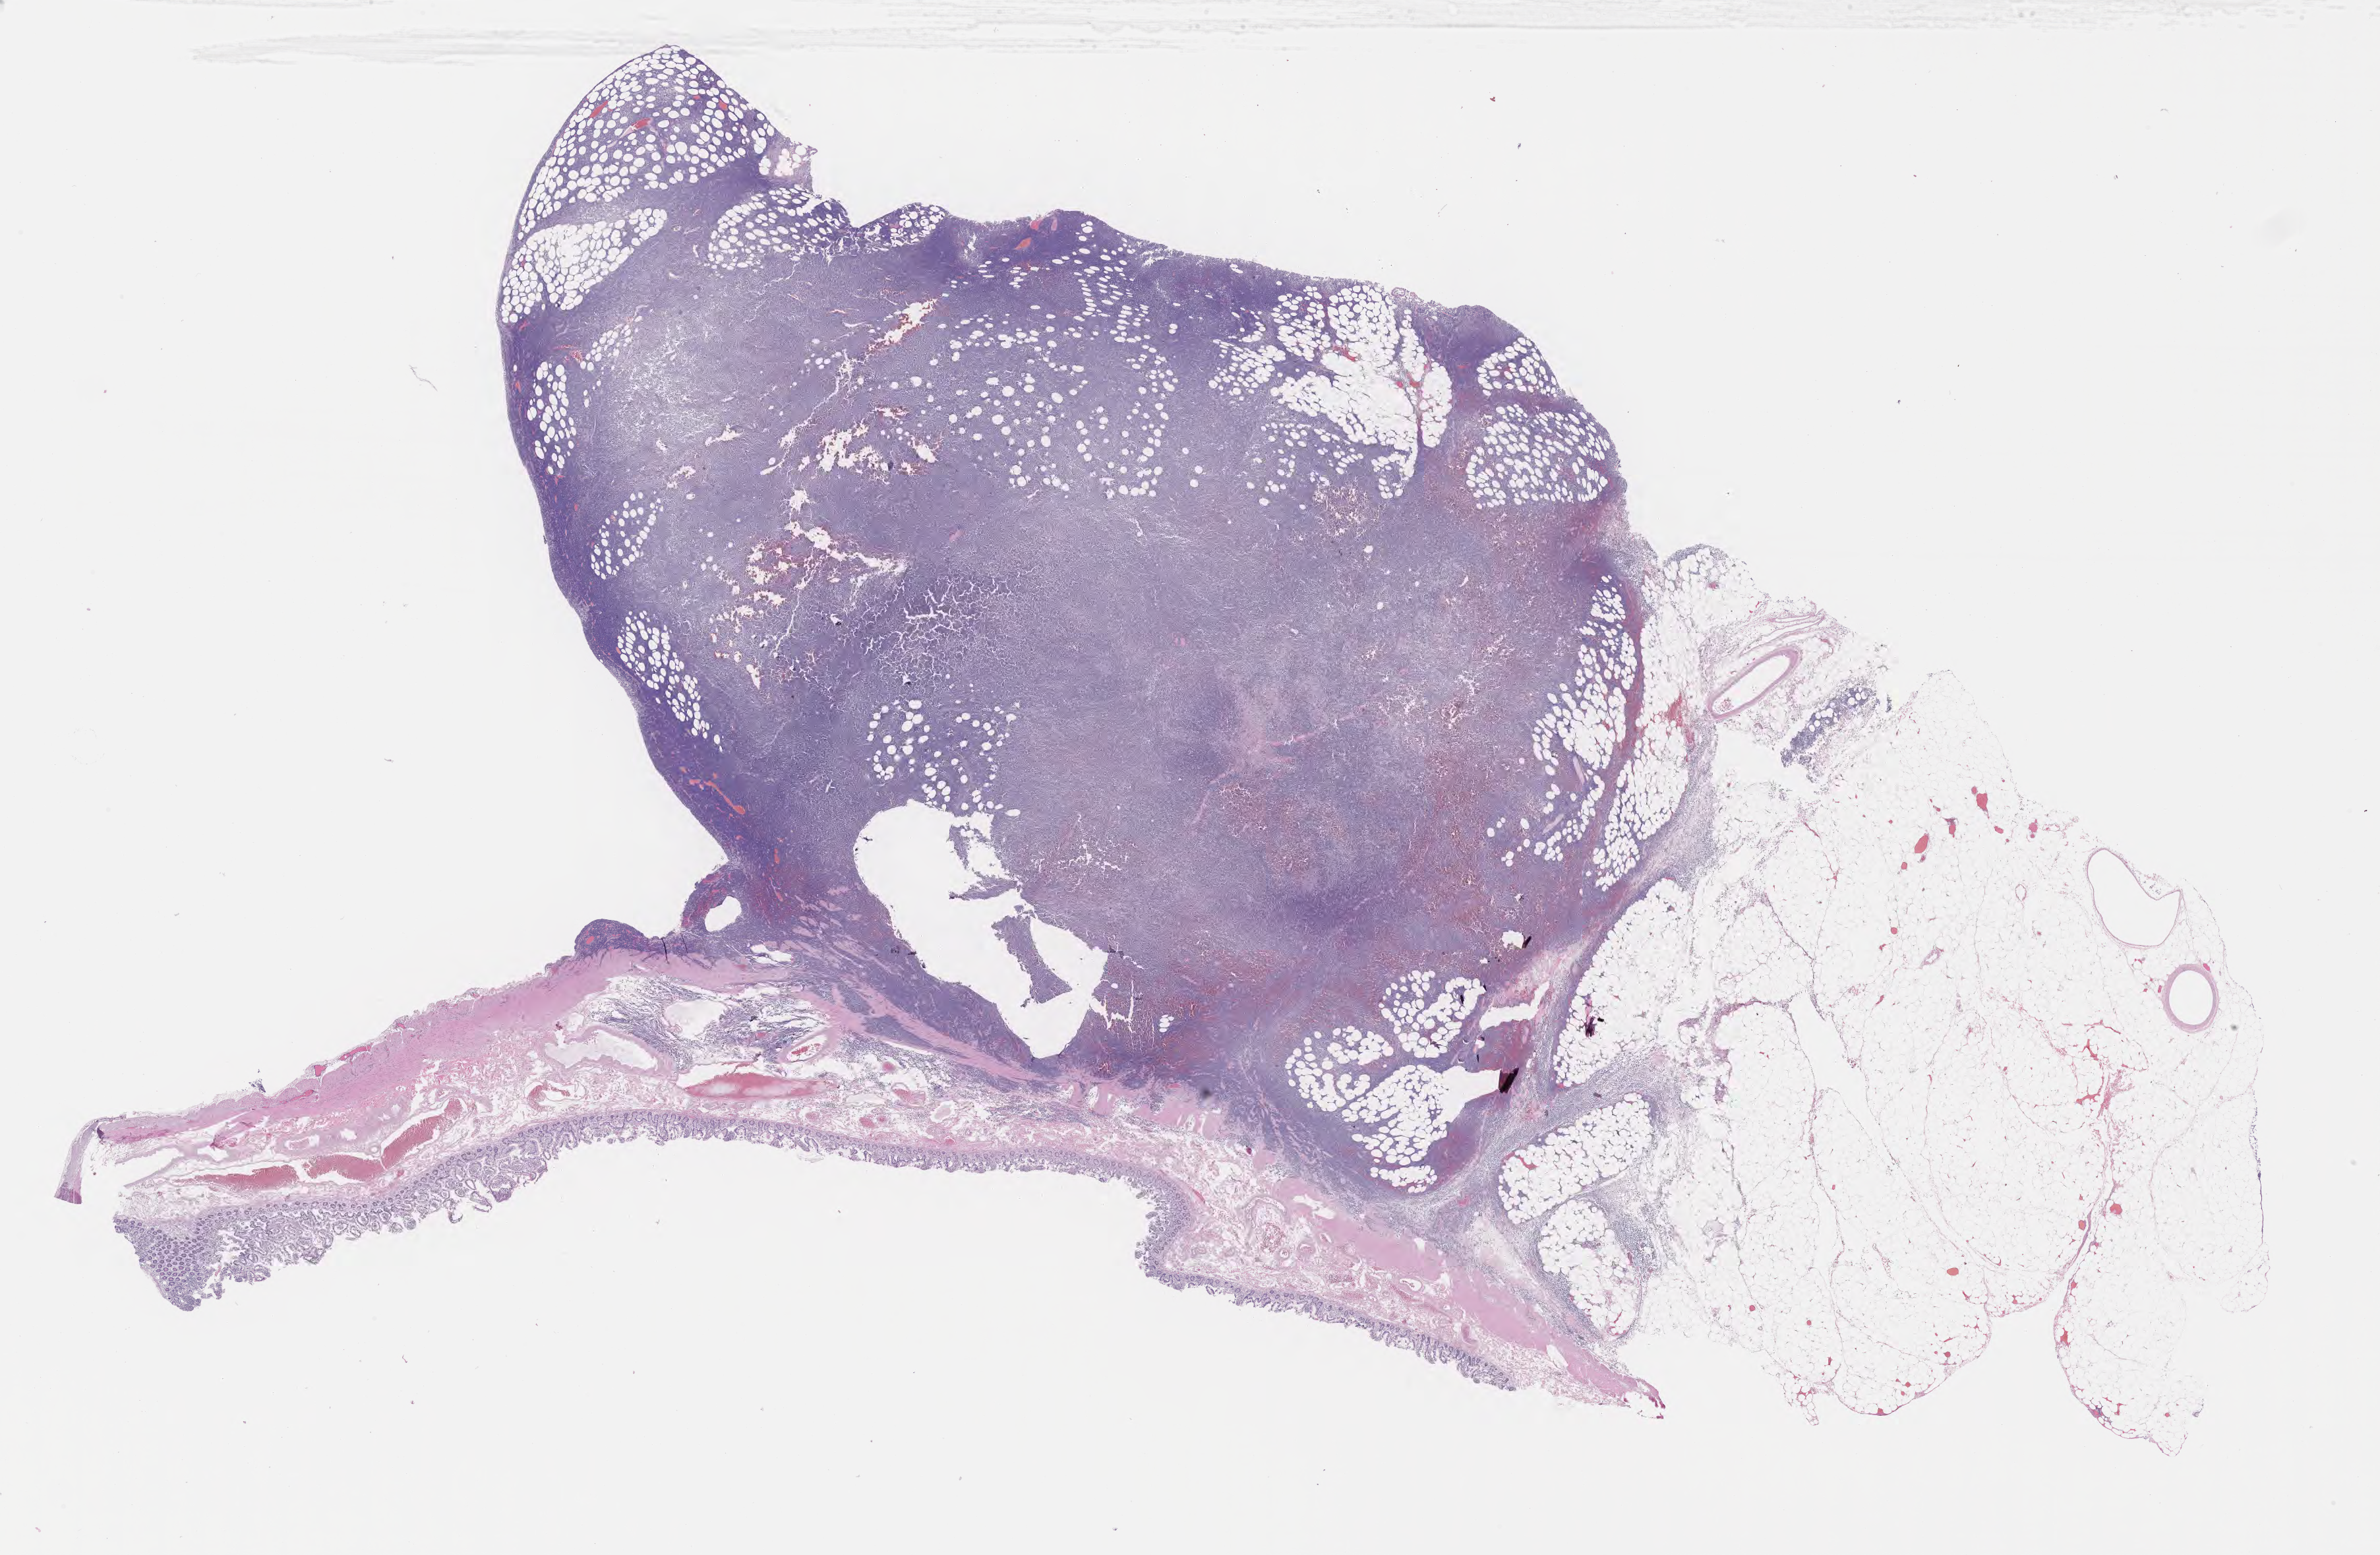
Digitized haematoxylin and eosin-stained section — low-resolution overview of the scanned area, about 29.2 x 19.1 mm. Specimen: tumor tissue. Anatomic site: small intestine. Male patient, aged 49.
Diagnosis: Burkitt lymphoma, NOS.